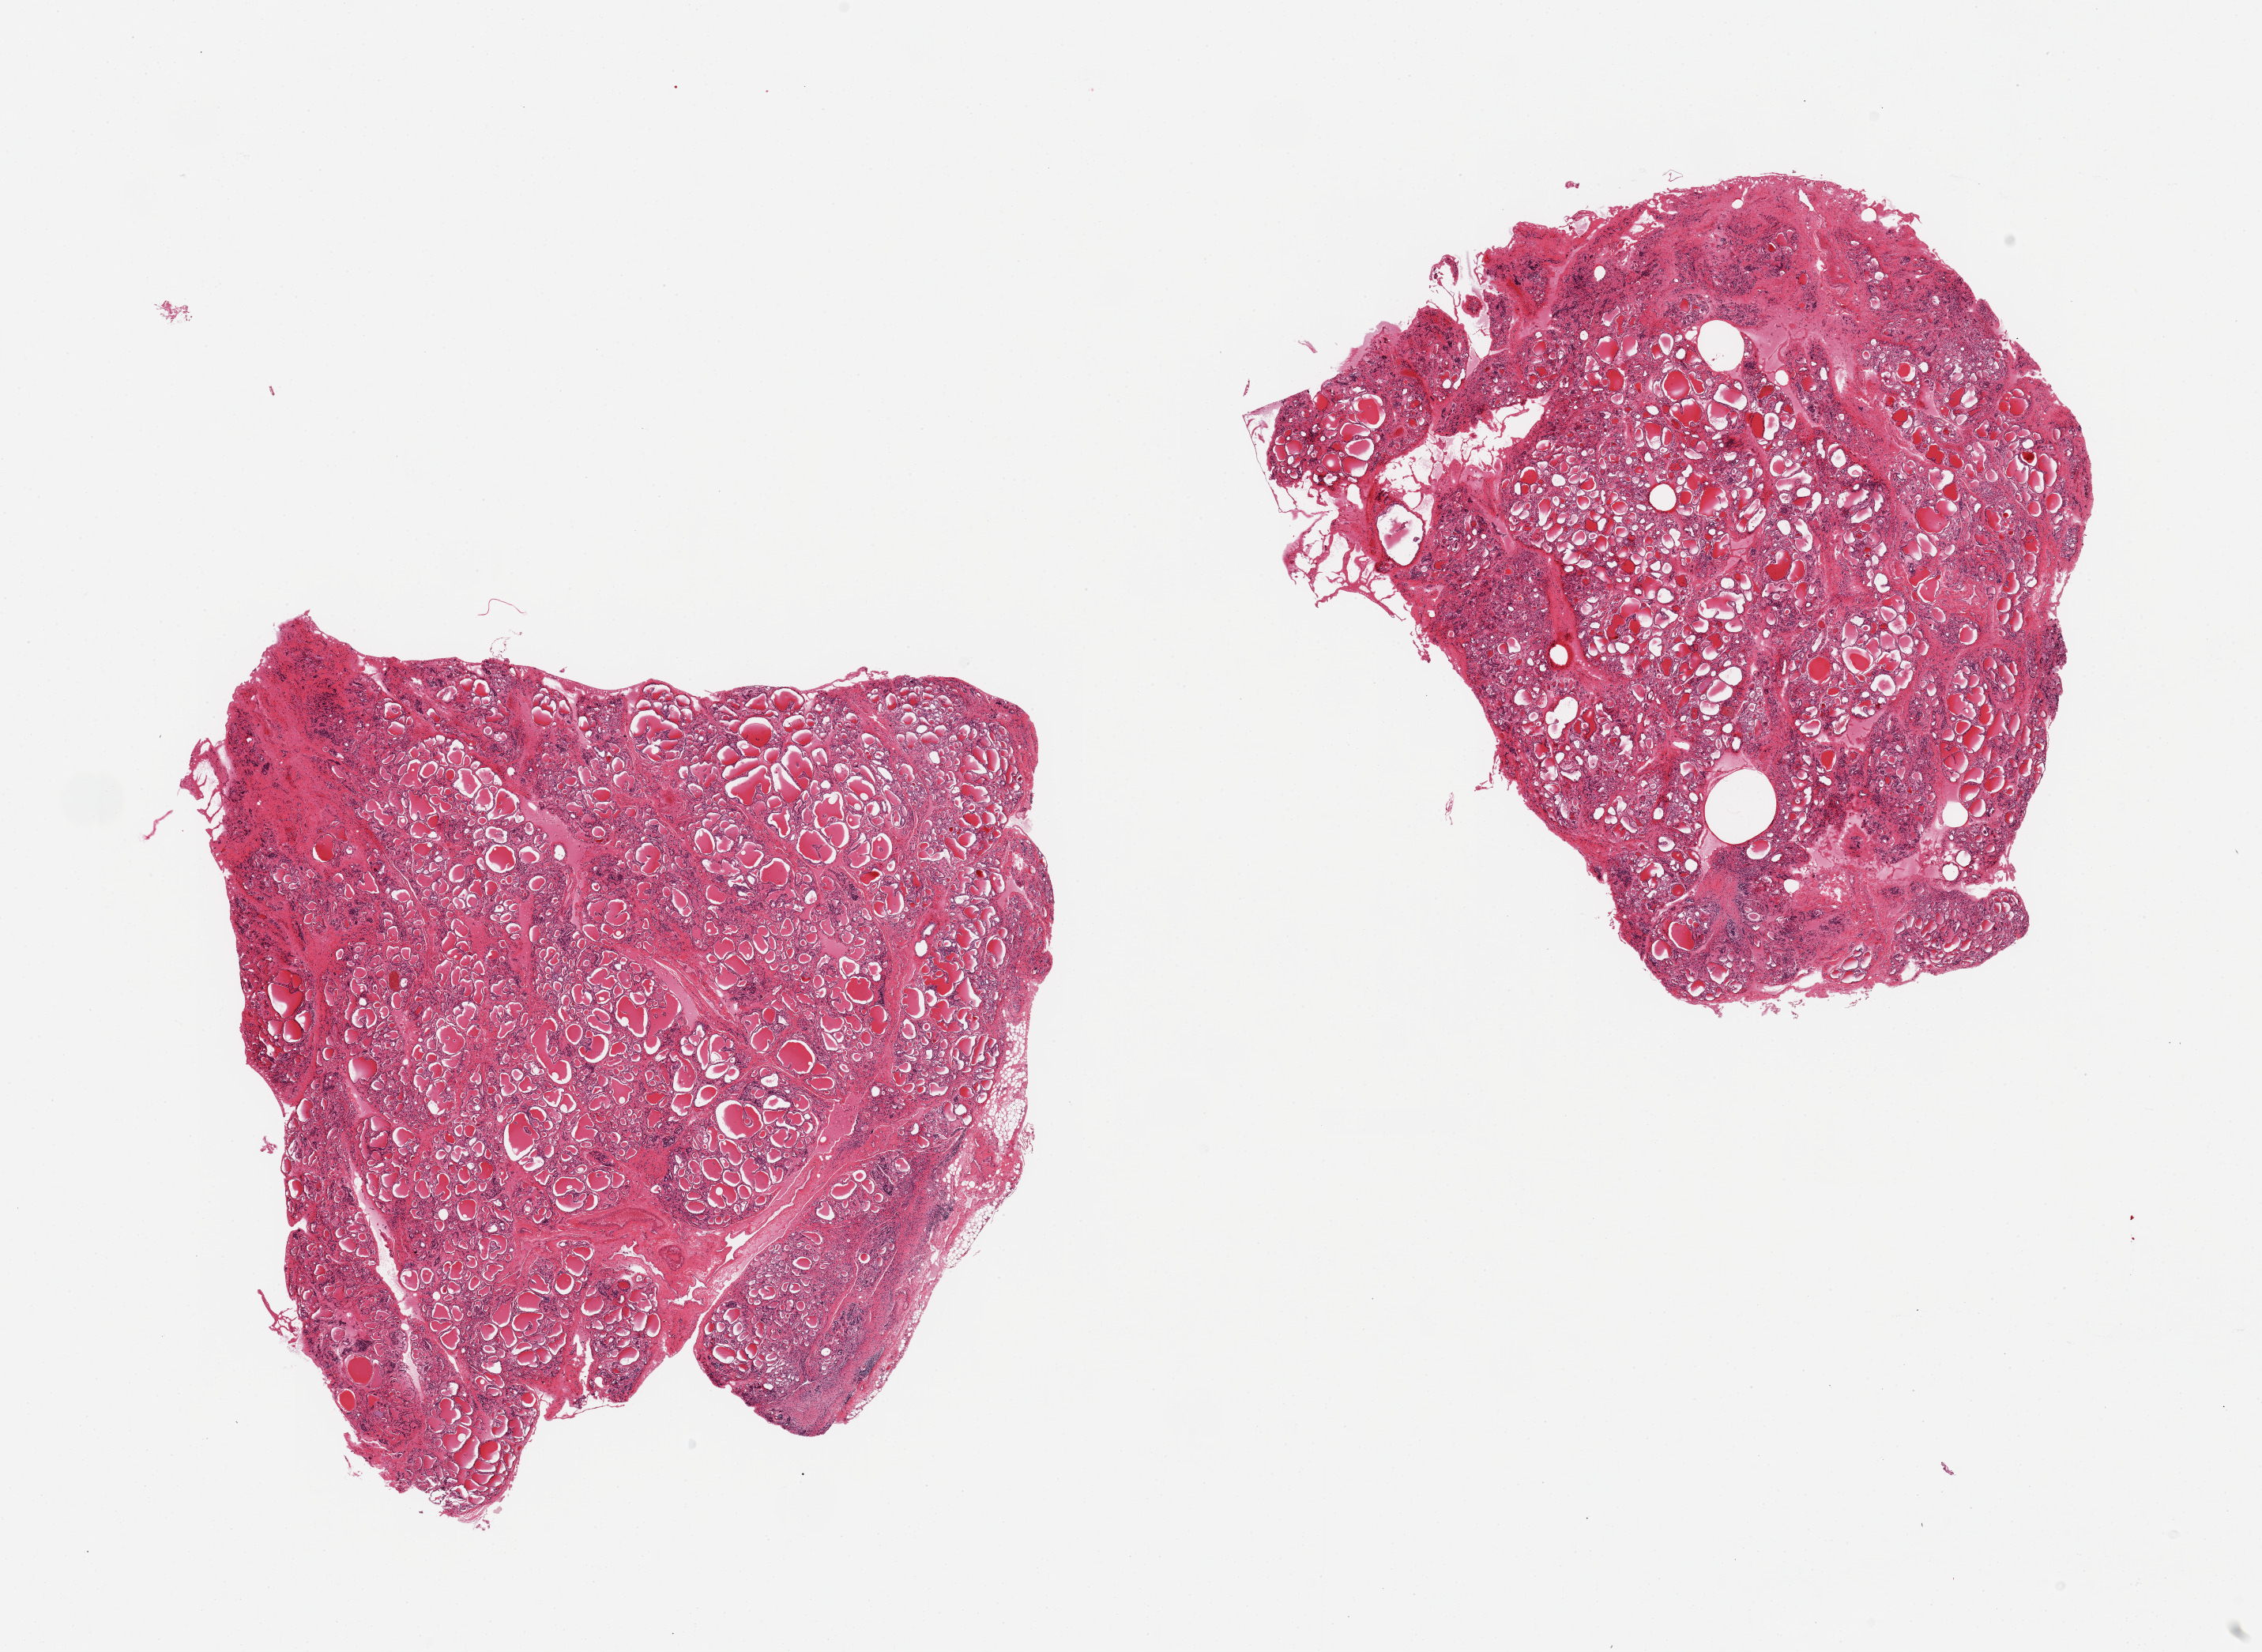
Digitized hematoxylin and eosin (H&E)-stained section, brightfield, whole scanned area (about 22.6 x 16.5 mm, acquisition: 20x scan) shown as a low-resolution overview, PAXgene-fixed paraffin-embedded (PFPE) section, target tissue: thyroid, donor tissue sample. Female donor.
Pathologist's review note for this sample: 2 pieces; focal atrophy & fibrosis.